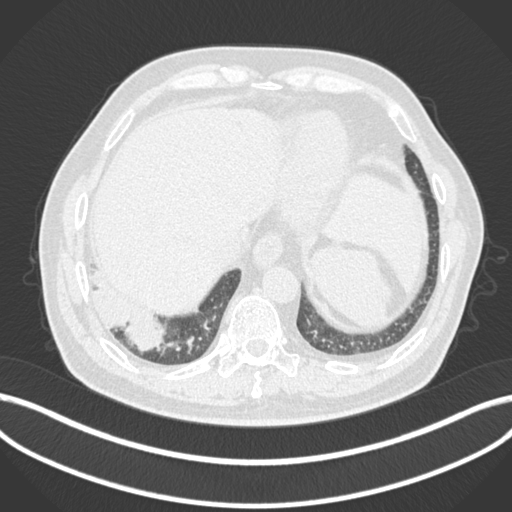
Chest CT, one axial slice. Slice 21 of 200 in the series (ordered by position). 120 kVp. Lung window (W 1500 / L -600 HU). 1 mm slice thickness. 512 × 512 image matrix. Male patient, age 59 years.
Annotated regions visible in this slice (rectangle marked by the reading radiologist):
- lung tumour (recorded histology: adenocarcinoma): bounding box (x1, y1, x2, y2) in pixels: (89, 278, 166, 355)